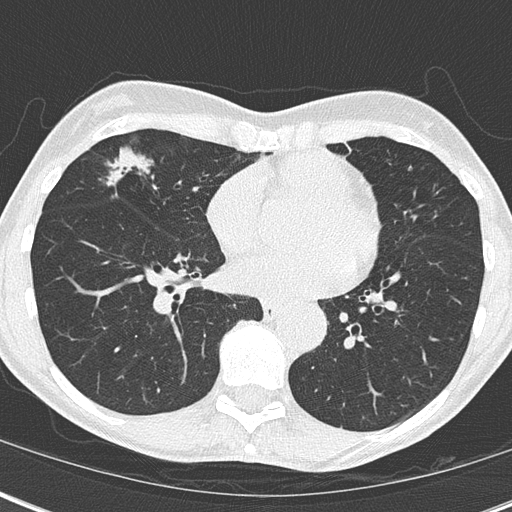
Axial slice from a low-dose chest CT screening exam. Third screening round (two years after baseline). Lung window (W 1500 / L -600 HU). Slice 103 of 173 in the series. Female participant, aged 67 years at enrolment. Current smoker at enrolment.
Expert reader's lesion annotation, bounding box <93,141,192,228> (left, top, right, bottom; pixels). The exam's reader record, not a measurement of the box and not confirmed to be the same lesion: non-calcified nodule or mass ≥4 mm, right middle lobe, 32 × 17 mm, mixed attenuation, pre-existing on the prior screen: yes; interval growth: yes. Participant outcome: lung cancer diagnosed 76 days after this screen — bronchiolo-alveolar adenocarcinoma, NOS, right middle lobe, well differentiated (G1), stage IA (AJCC 6th edition), 25 mm at pathology.